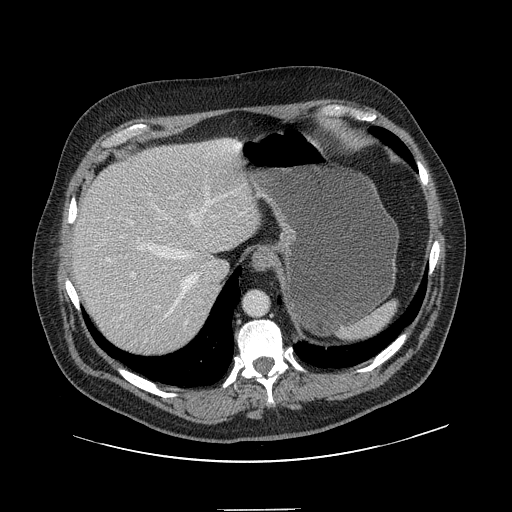
Contrast-enhanced abdominal CT, one axial slice. Position 117 of 154 along the scan axis. Intravenous contrast given. Soft-tissue window (W 400 / L 40 HU). 2.5 mm slice thickness. 512 × 512 image matrix, field of view 451 × 451 mm. Male patient, age 61 years. From the clinical record (not read from this slice): diagnosis: colorectal cancer liver metastases, imaged before liver resection; multiple liver metastases: yes; largest metastasis: 2.6 cm; chemotherapy before resection: no.
Structures marked on this image (outlined manually by an expert reader):
- hepatic veins: bounding box <137,192,234,317> (left, top, right, bottom; pixels)
- liver: <71,140,261,357>
- planned liver remnant (the part of the liver to remain after resection): <72,143,261,353>
- portal vein (with intrahepatic branches): <120,217,213,308>